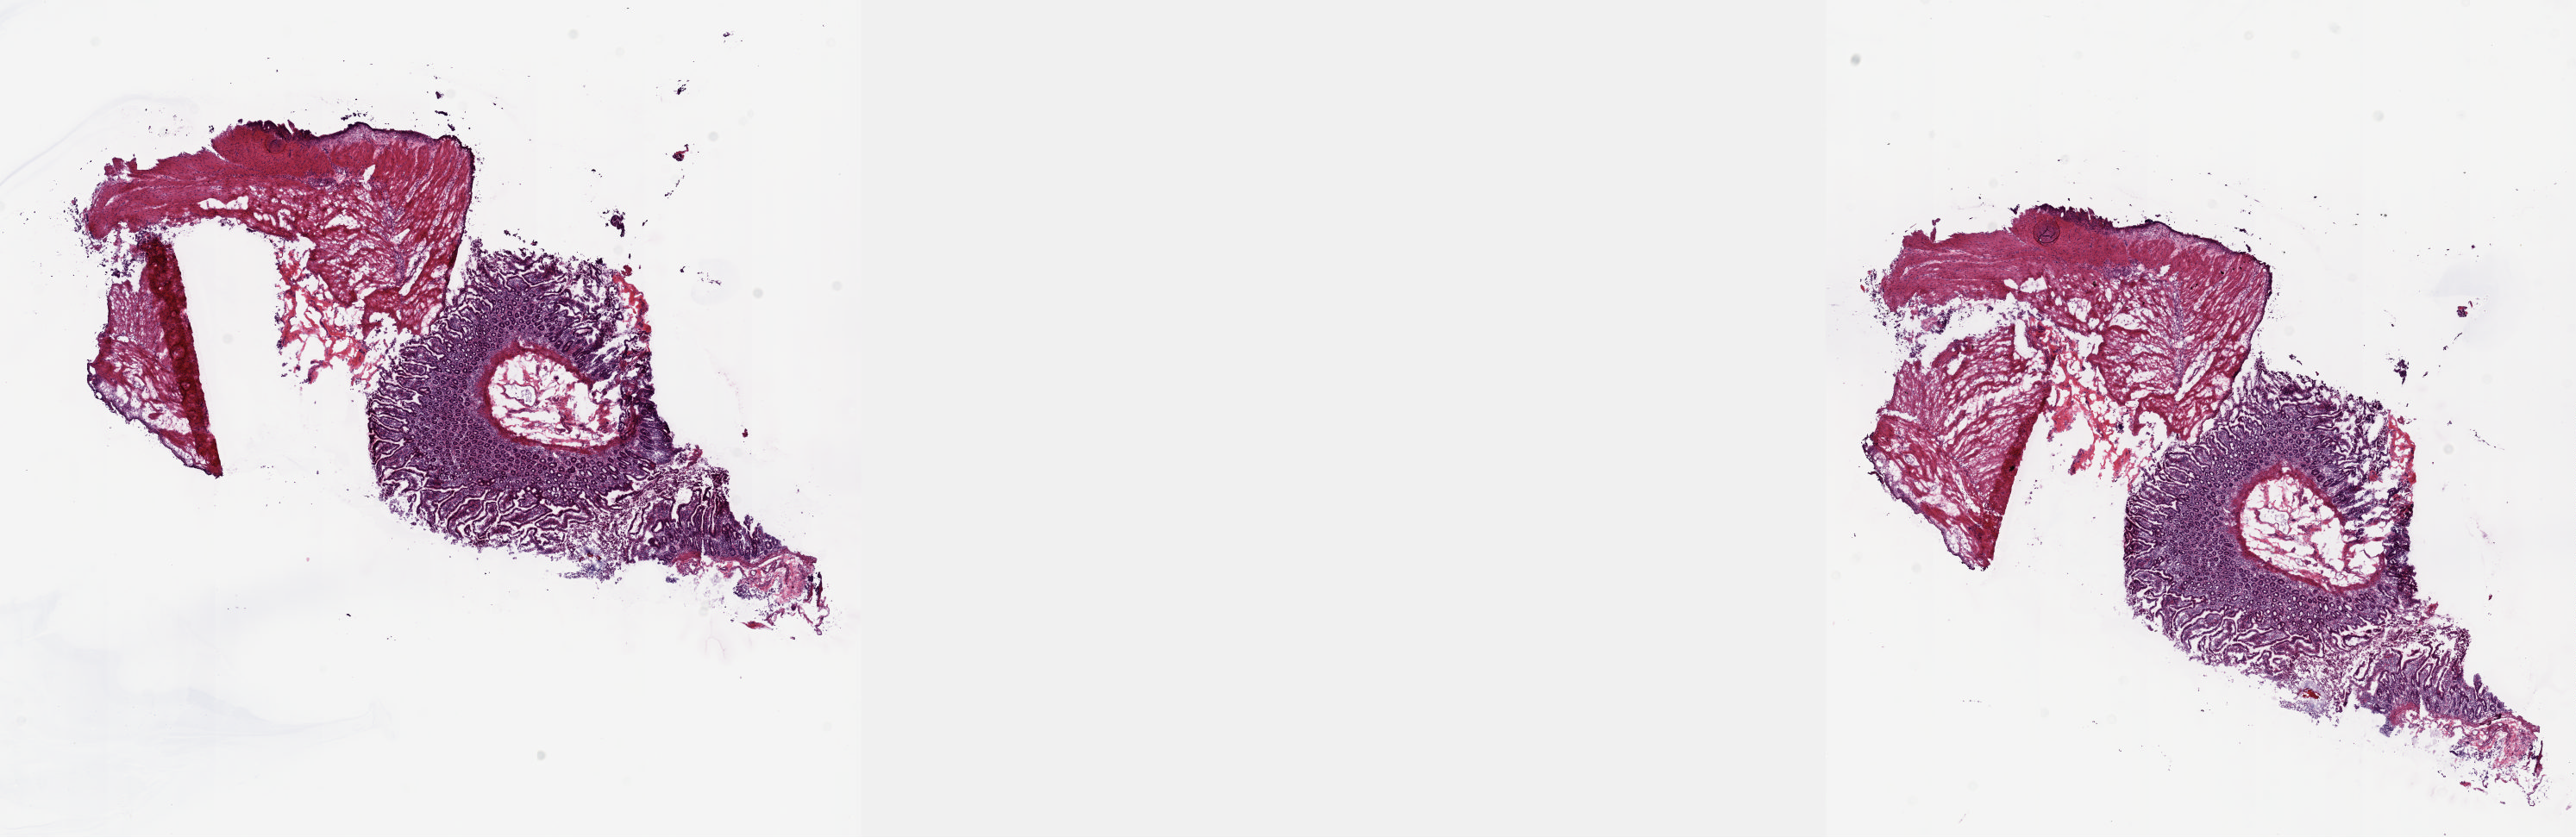
H&E-stained whole-slide image — shown as a low-resolution overview of the whole scanned area (about 24.1 x 7.8 mm); frozen section from the top of the tissue portion; solid tissue normal (non-tumour tissue) sample from the pancreas. Female, age 41 years at initial diagnosis. Pathologist review of this section (percent, as recorded): tumour cells 0%, tumour nuclei 0%, normal cells 100%, stromal cells 0%, necrosis 0%. Infiltration values recorded for this section: lymphocyte infiltration 0%, monocyte infiltration 0%, neutrophil infiltration 0%.
This section: solid tissue normal (non-tumour) sample from the same patient. Patient diagnosis: Infiltrating duct carcinoma, NOS (head of pancreas).